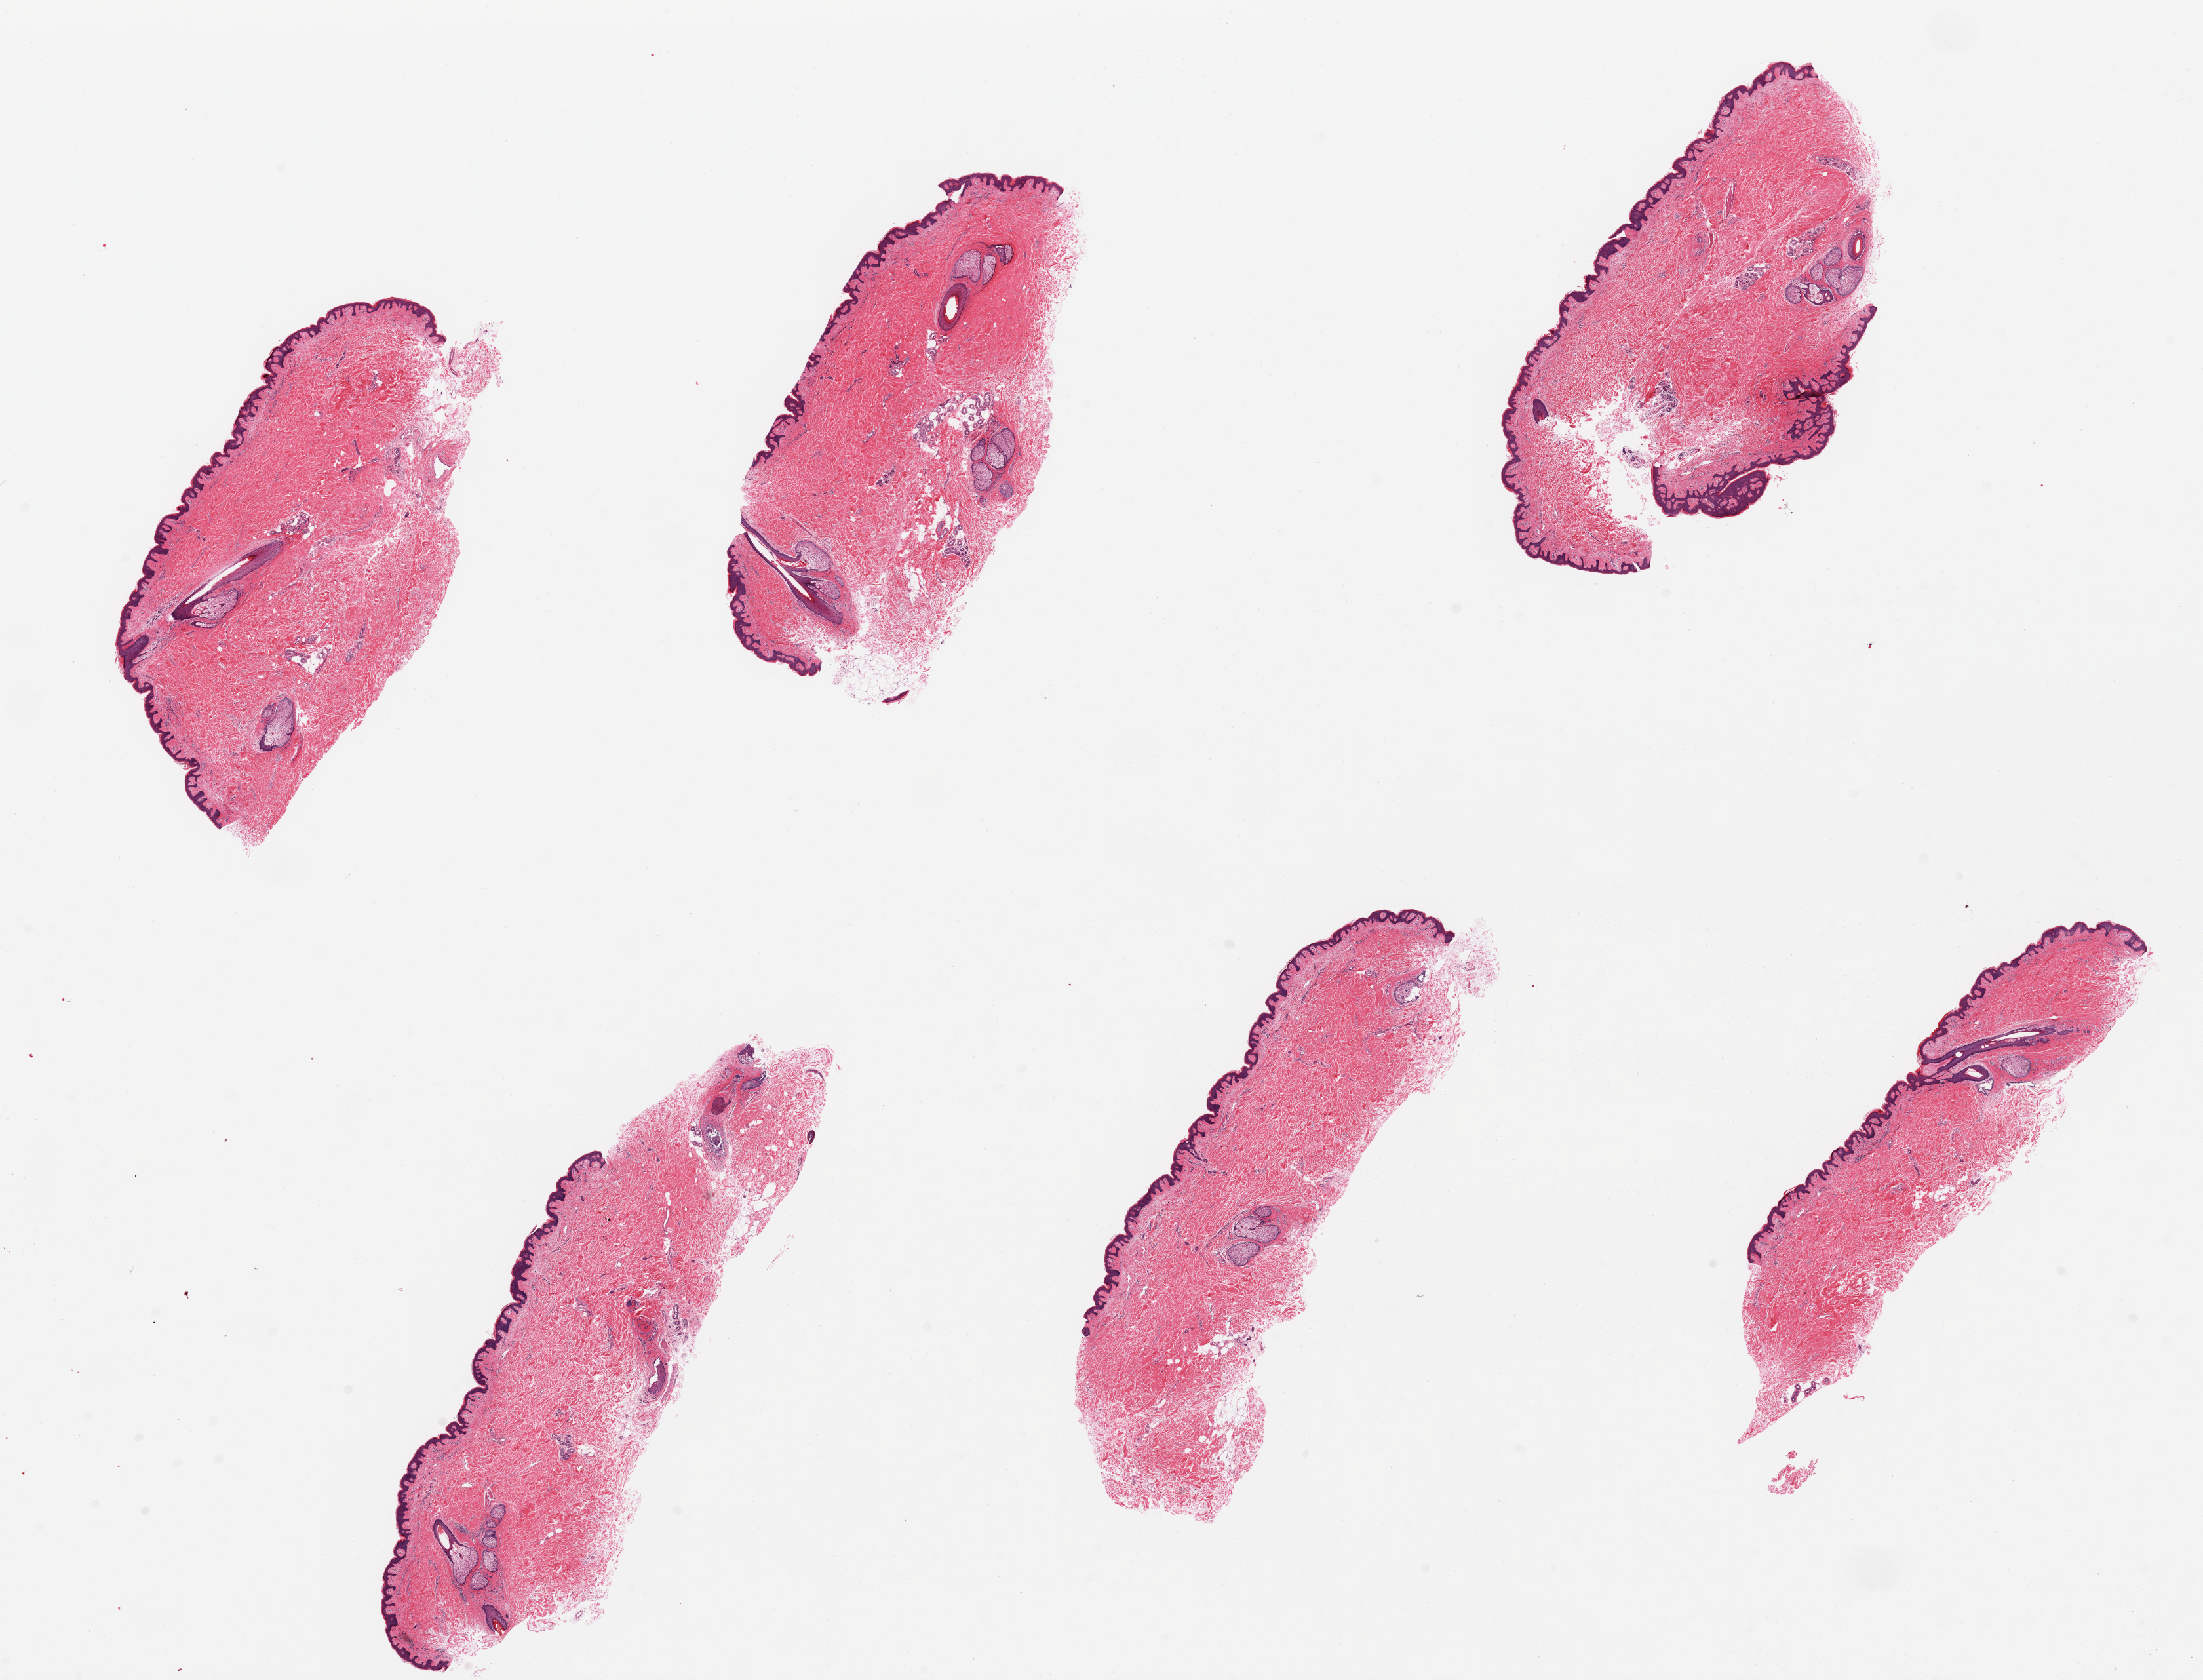
Hematoxylin and eosin (H&E) whole-slide image — a low-resolution overview of the entire scanned area, about 26.6 x 20.3 mm. PAXgene-fixed, paraffin-embedded tissue. Target tissue: skin of suprapubic region. Tissue donor sample. Donor: male.
Reviewer comment on this tissue sample: 6 pieces; well trimmed.